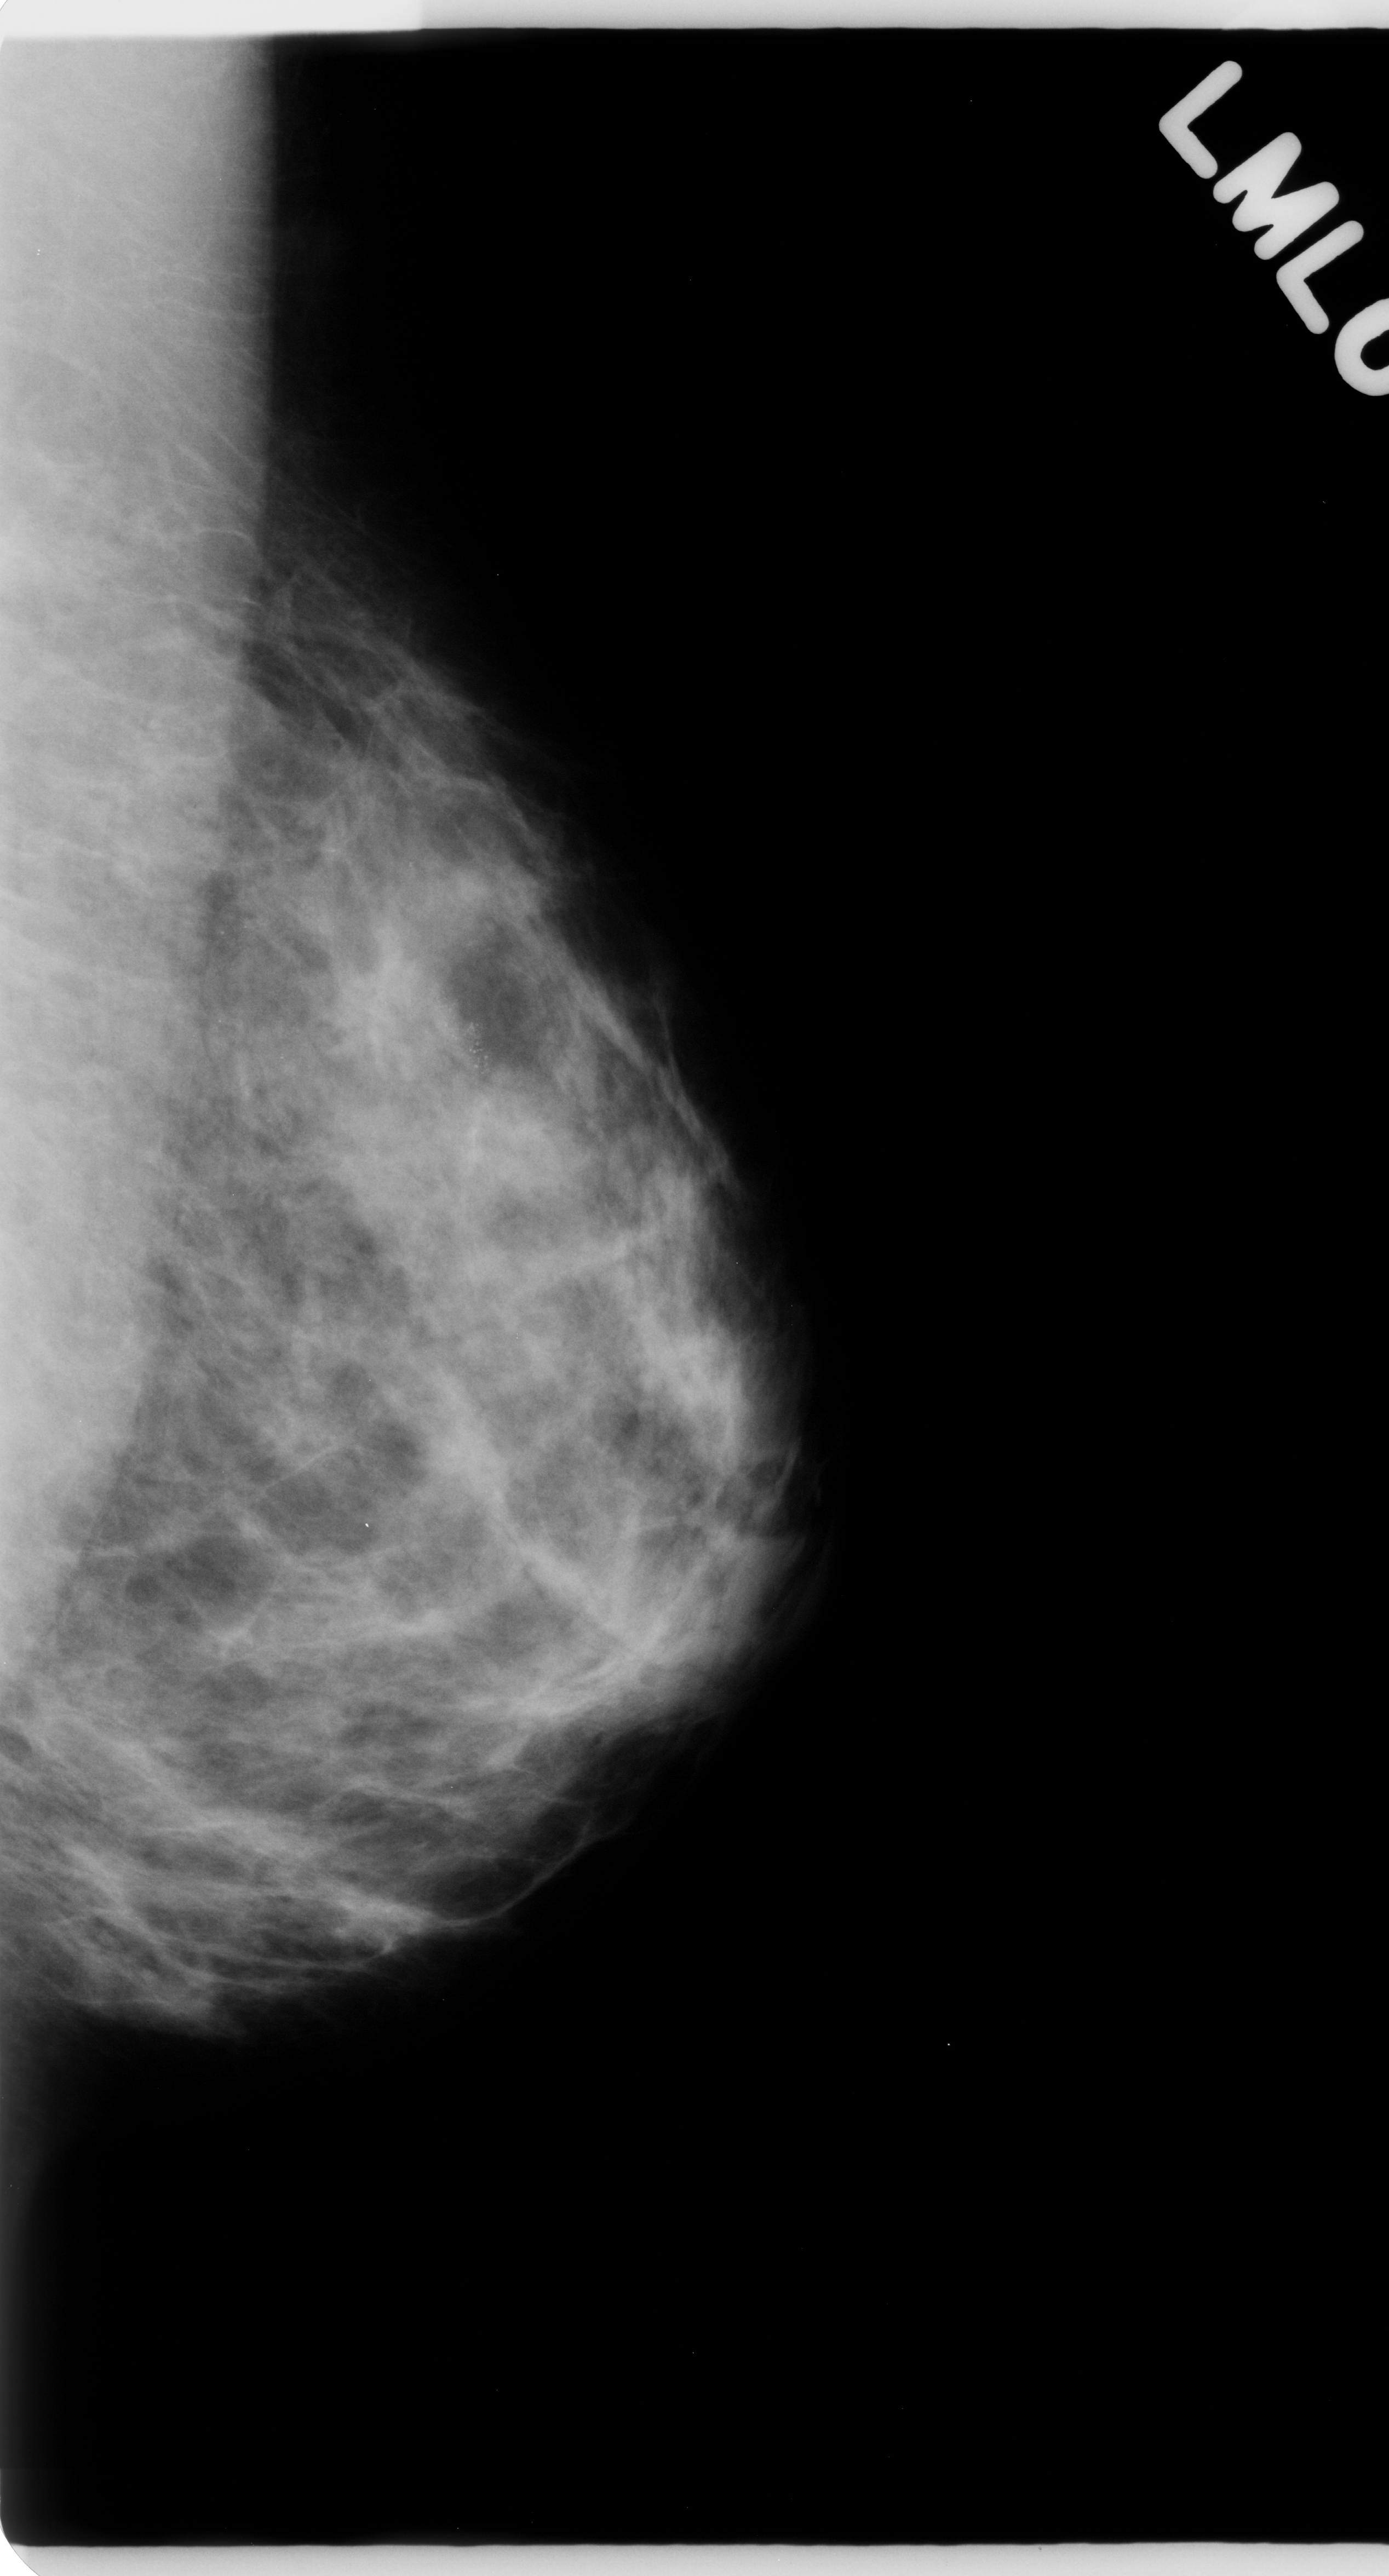
Scanned film-screen mammogram; left breast; mediolateral oblique (MLO) view; BI-RADS breast density category 2 (scale 1–4); 1389 × 2576 image matrix.
Expert-marked regions of interest on this film, with their recorded descriptors:
- calcifications, morphology pleomorphic, distribution clustered; BI-RADS assessment category 5; pathology (as recorded): malignant: bounding box [x1, y1, x2, y2] px = [302, 906, 549, 1193]